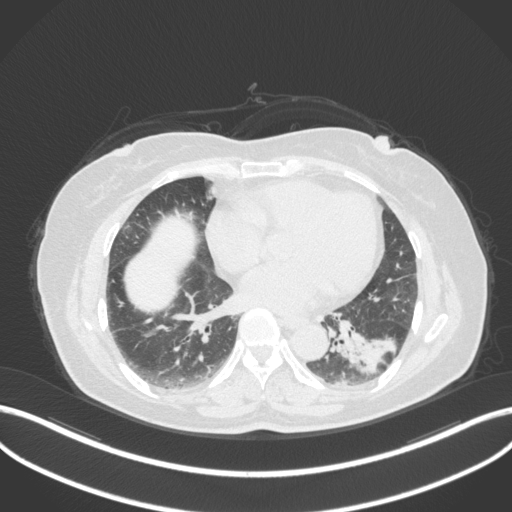
Chest CT, one axial slice. Slice 152 of 307 in the series (ordered by position). Reconstruction kernel B31f. 120 kVp. Lung window (W 1500 / L -600 HU). 1 mm slice thickness. 512 × 512 image matrix. Patient: female, 59 years. From the clinical record (not read from this slice): clinical TNM (as recorded): T2a N0 M0.
Outlined on this slice (bounding box drawn by a radiologist):
- lung tumour (recorded histology: adenocarcinoma): bounding box <329,318,400,379> (left, top, right, bottom; pixels)